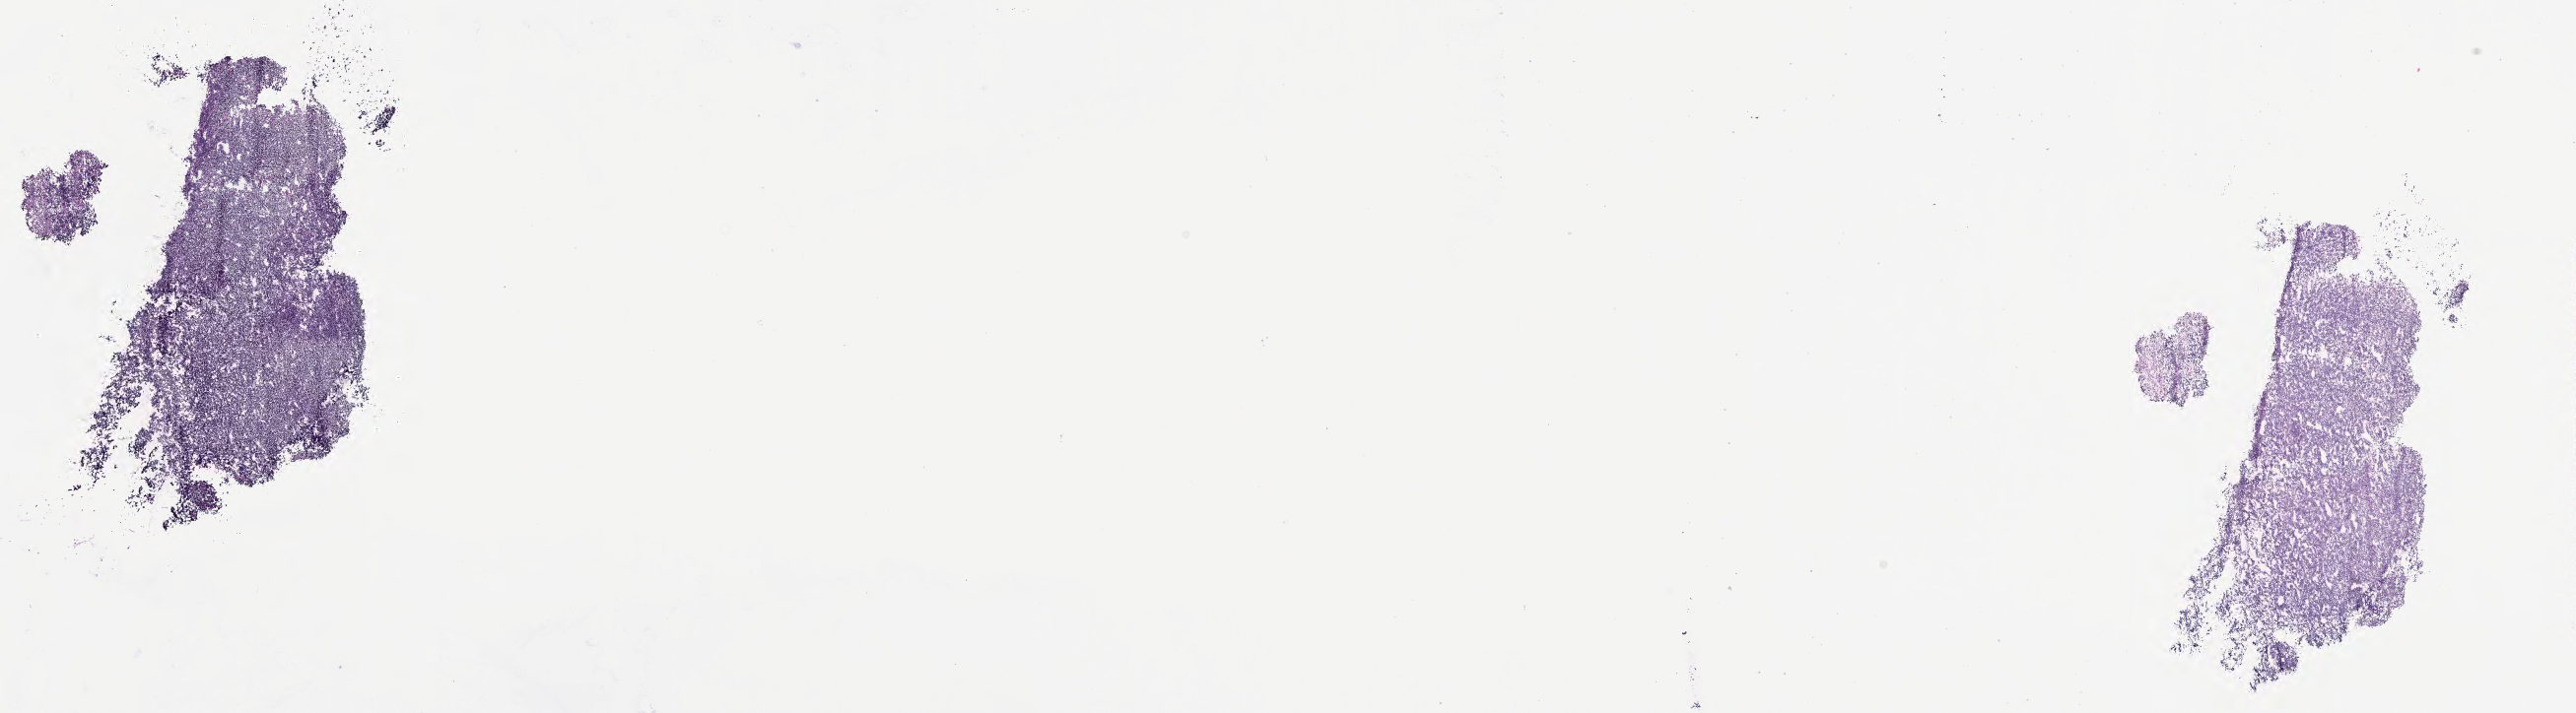
Haematoxylin and eosin whole-slide image of tumor tissue from the thymus, a low-resolution overview of the entire scanned area, about 21.1 x 5.8 mm, frozen section (OCT-embedded). Patient female; age 182 months (15 years 2 months).
- recorded diagnosis: Thymoma, NOS